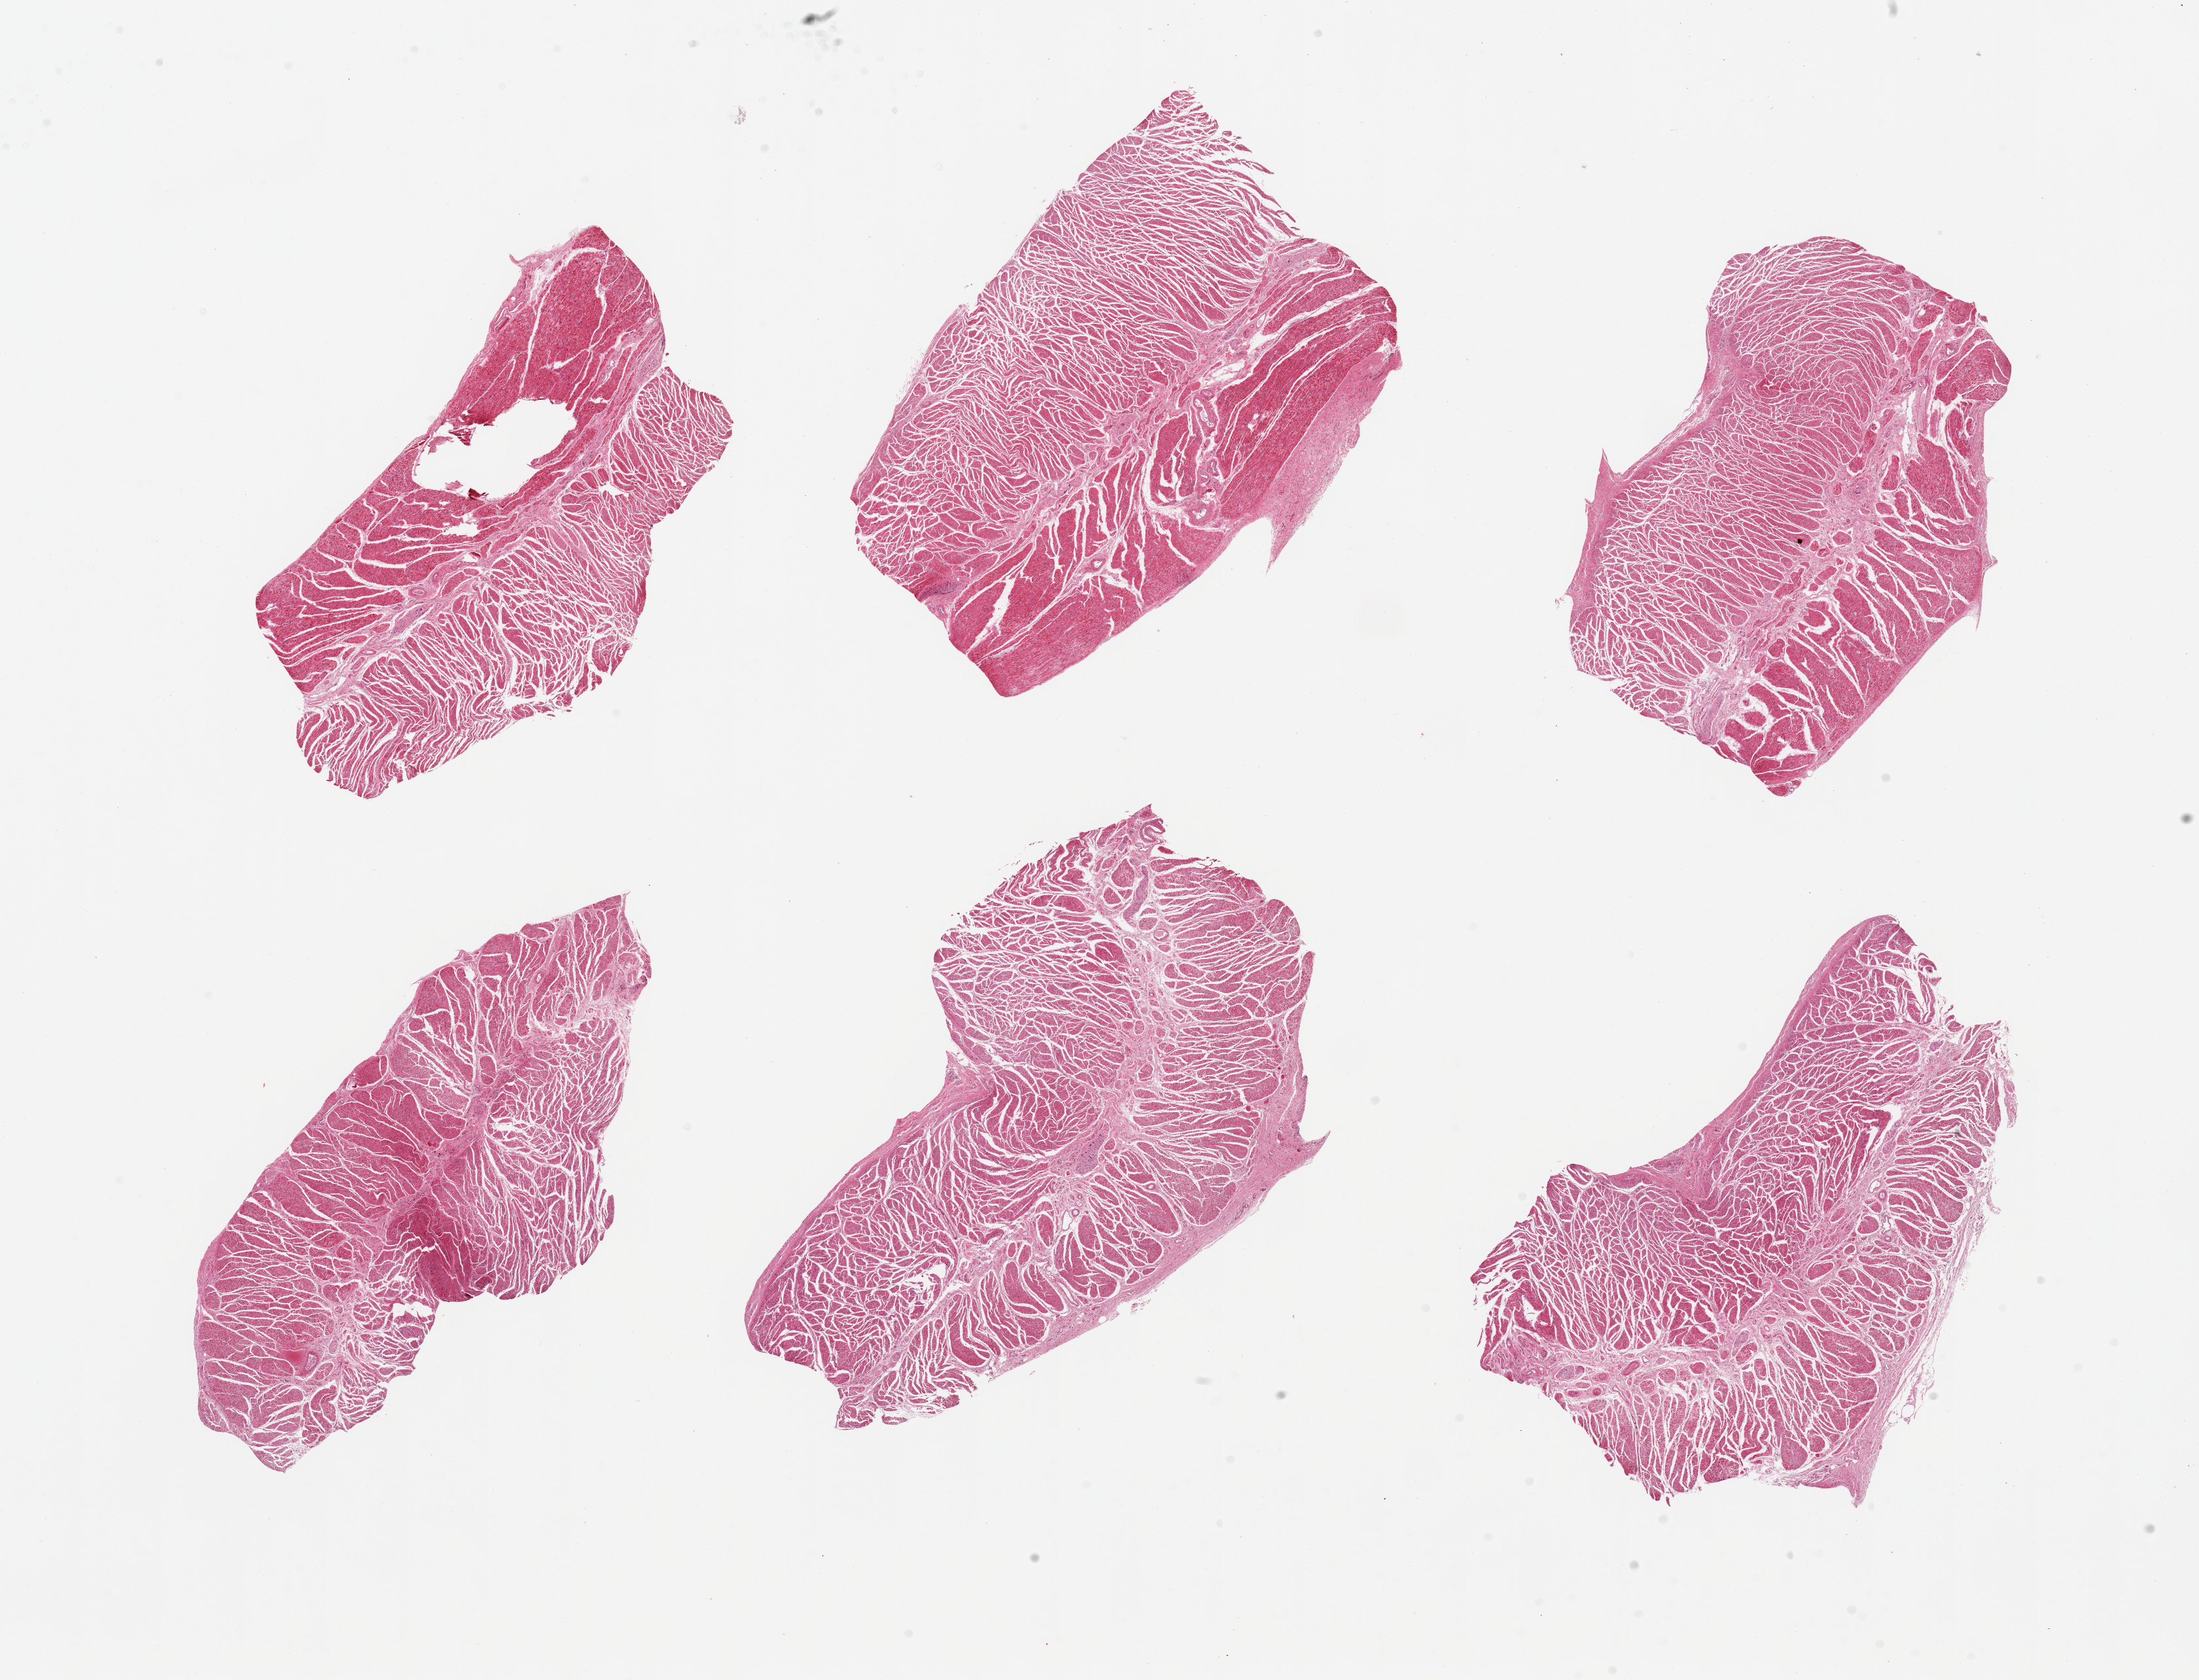
Digitized H&E-stained section — whole scanned area (about 26.6 x 20.3 mm, slide scanned at 20x) shown as a low-resolution overview, PAXgene-fixed paraffin-embedded (PFPE) section, target tissue: esophageal muscle, donor tissue sample. Donor: female.
* pathologist's review note for this sample: 6 pieces, all target muscularis